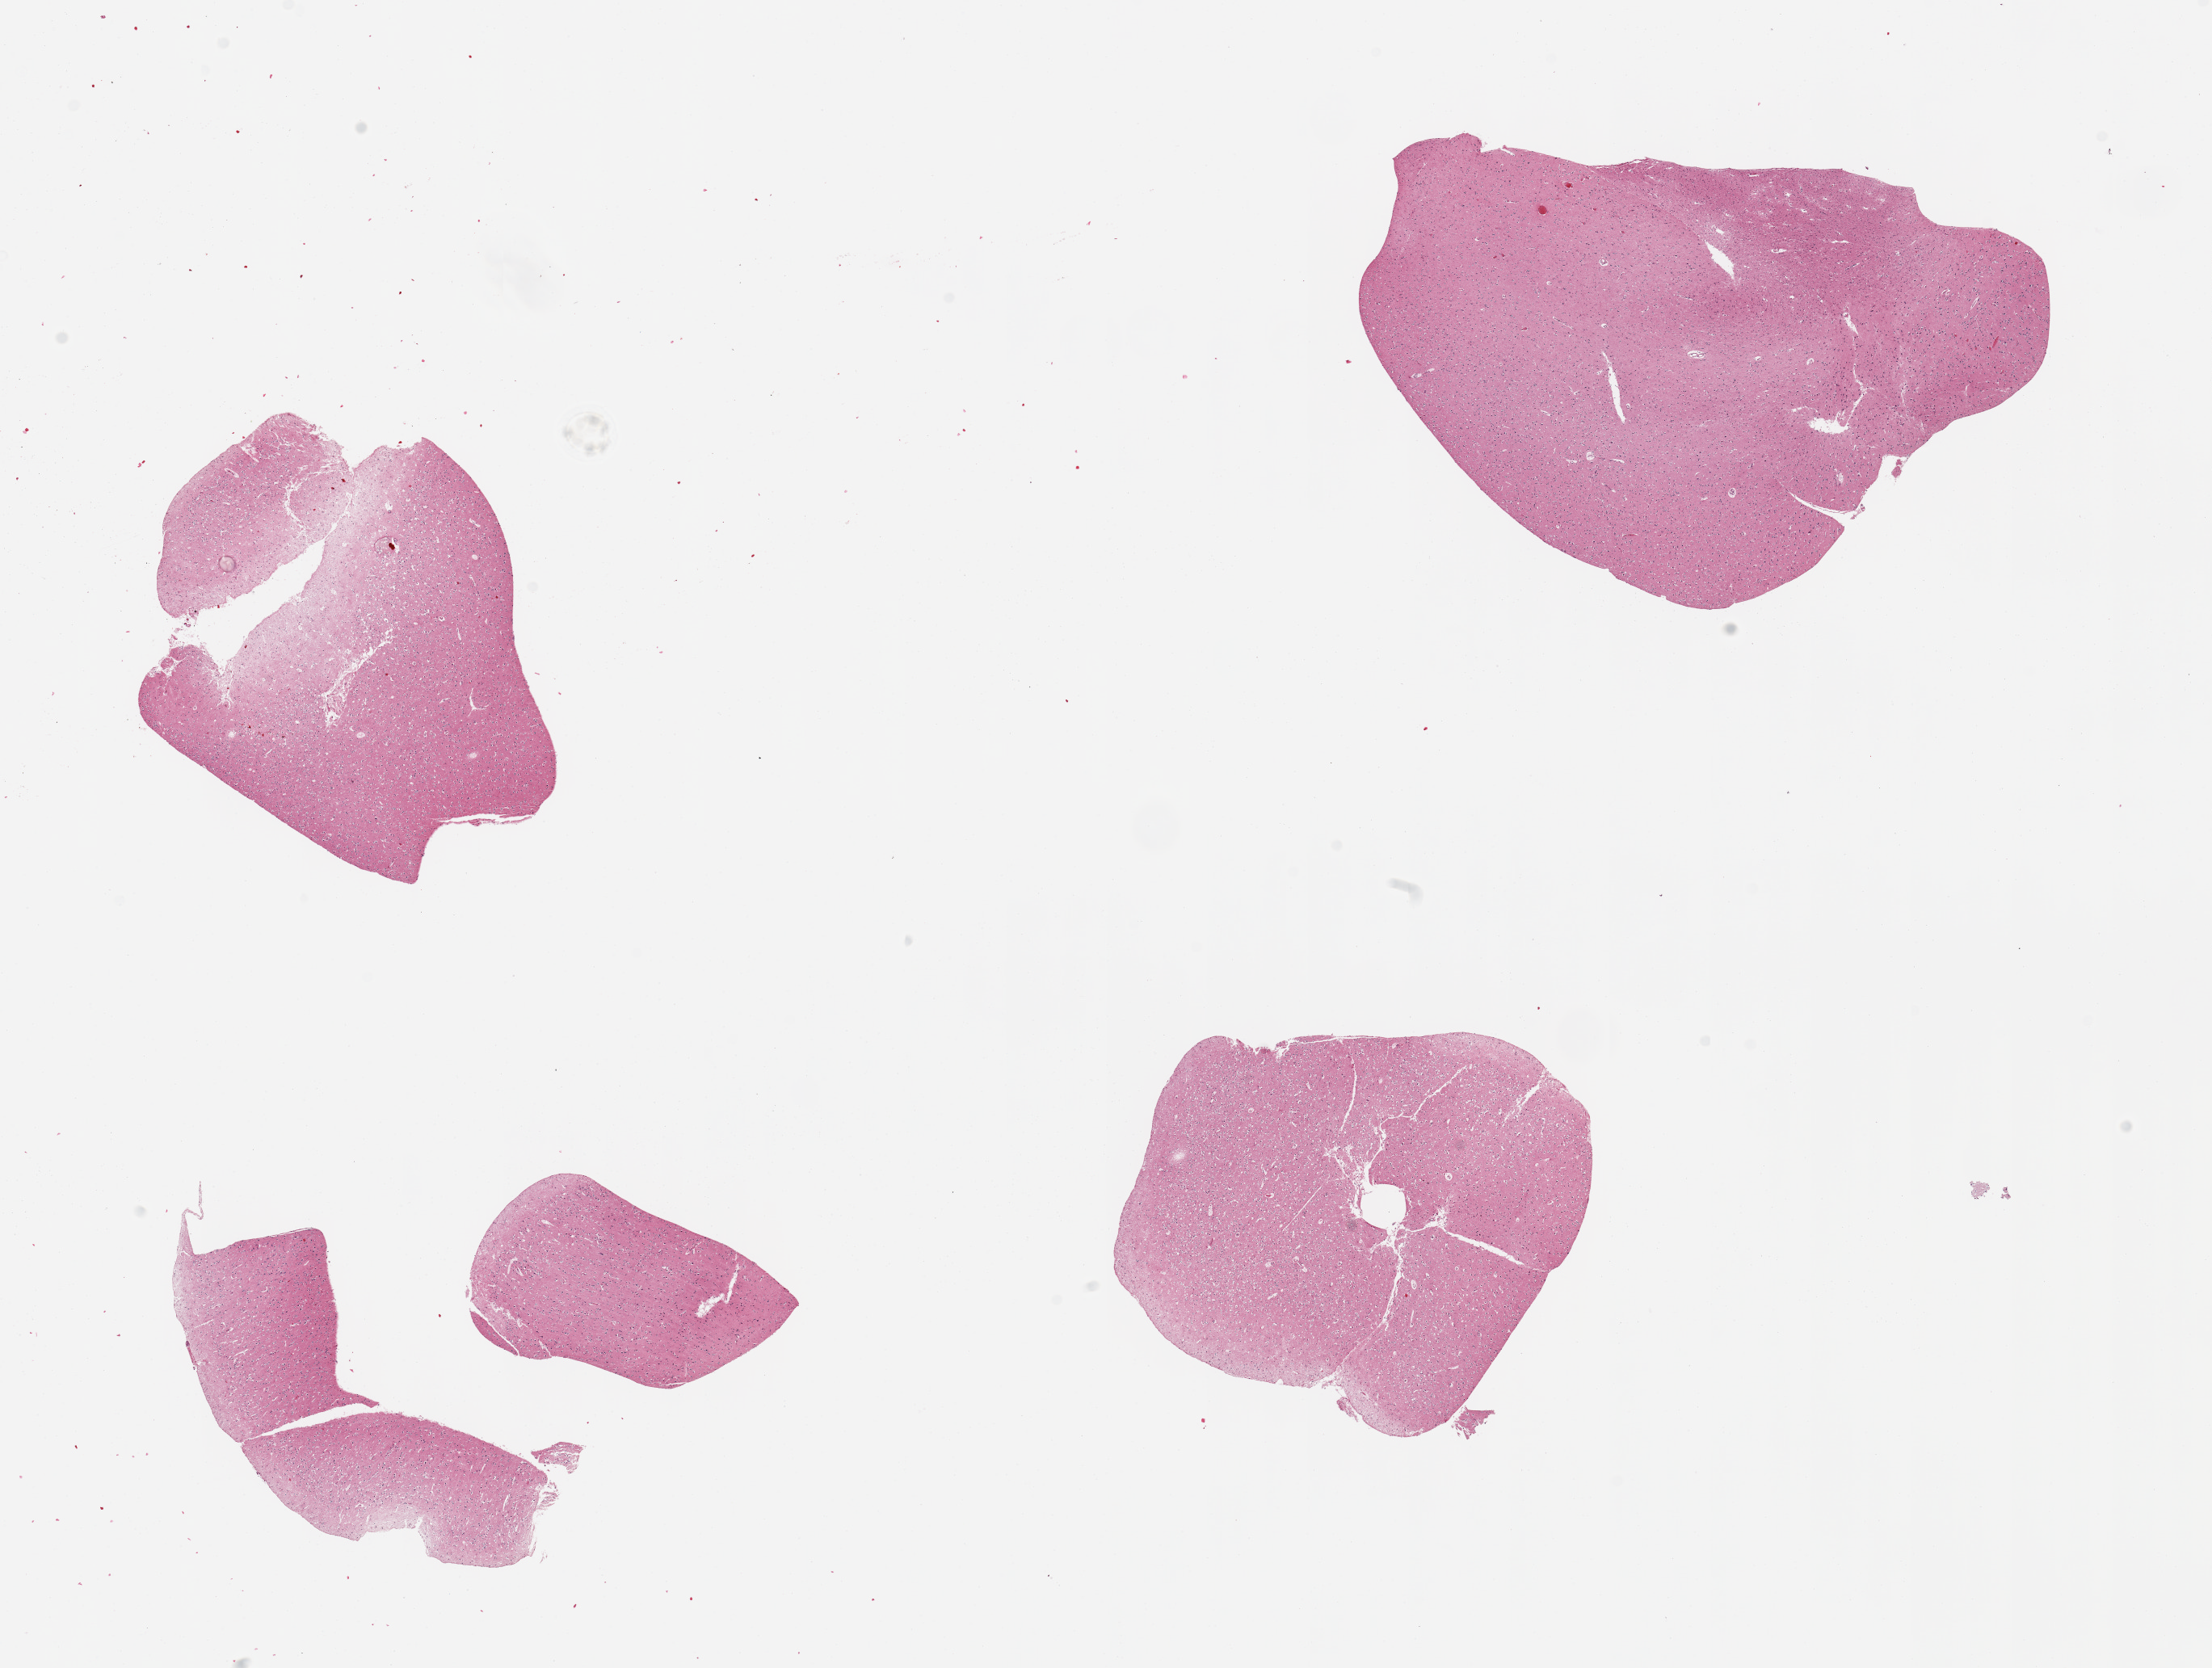
Haematoxylin and eosin whole-slide image, brightfield, low-resolution overview of the scanned area, about 21.7 x 16.3 mm (from a 20x scan). PAXgene-fixed, paraffin-embedded tissue. Section of cerebral cortex (target tissue). Tissue donor sample. Donor: male.
- pathologist's review note for this sample: 4 pieces with fragmentation